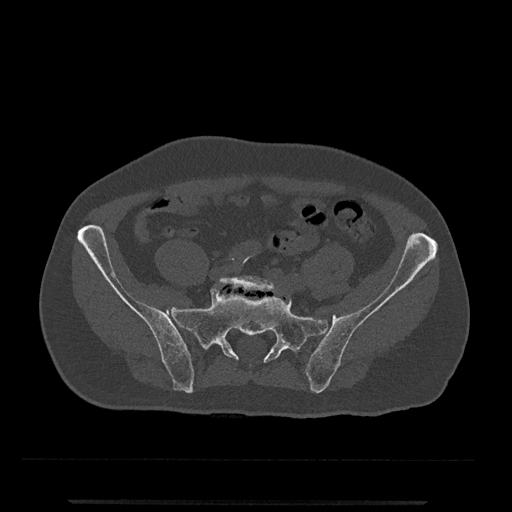
CT including the spine, one axial slice; reconstruction kernel Br40s/3; bone window (W 1800 / L 400 HU); 512 × 512 image matrix. Male patient, age 63 years. From the clinical record (not read from this slice): primary cancer: prostate.
Structures marked on this image (semi-automatically segmented with operator editing):
- L5 vertebra: box from (x=218, y=275) to (x=277, y=292) px